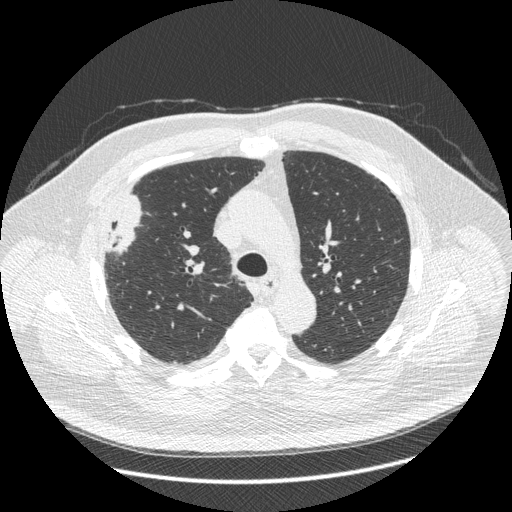
Chest CT (low-dose screening protocol), one axial image, third annual screen, lung window (W 1500 / L -600 HU), 1.25 mm slice thickness, standard (soft-tissue) reconstruction kernel (STANDARD), slice 128 of 426 in the series. Male, age 66 years at enrolment. Current smoker at enrolment.
Lesion marked by an expert reader, bounding box <87,199,147,268> (left, top, right, bottom; pixels). The exam's reader record, not a measurement of the box and not confirmed to be the same lesion: non-calcified nodule or mass ≥4 mm, right upper lobe, 48 × 25 mm, spiculated (stellate) margins, soft tissue attenuation, pre-existing on the prior screen: no. Official screen result: positive, other. Lung cancer was diagnosed 35 days after this screen: non-small cell carcinoma, right upper lobe, stage IV (AJCC 6th edition), 50 mm at pathology.